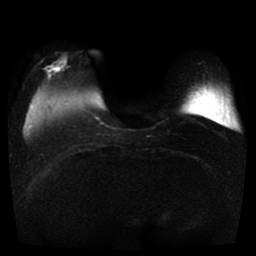
Breast MRI, one axial slice; slice 8 of 41 in the series (ordered by position); diffusion-weighted series; image 2 of 4 stored at this slice position (different b-values; order by instance number); 1.5 T; 5 mm slice thickness; 256 × 256 image matrix. Female patient.
Outlined on this slice (expert manual segmentation):
- tumour on diffusion-weighted imaging: bounding box <47,66,59,71> (left, top, right, bottom; pixels)